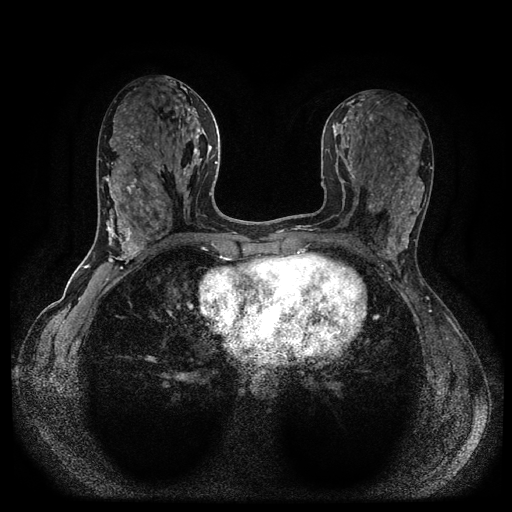
Breast MRI (dynamic contrast-enhanced, multi-phase), one axial slice; slice 48 of 116 in the series (ordered by position); dynamic contrast-enhanced series, time point 2 of 5 at this slice position (early post-contrast); 1.5 T; TE 2.6 ms, TR 5.4 ms; 512 × 512 image matrix, field of view 340 × 340 mm. Patient: female, 43 years.
Outlined on this slice (semi-automatically segmented with operator editing):
- breast lesion (labelled benign in the annotation): box from (x=366, y=199) to (x=382, y=218) px